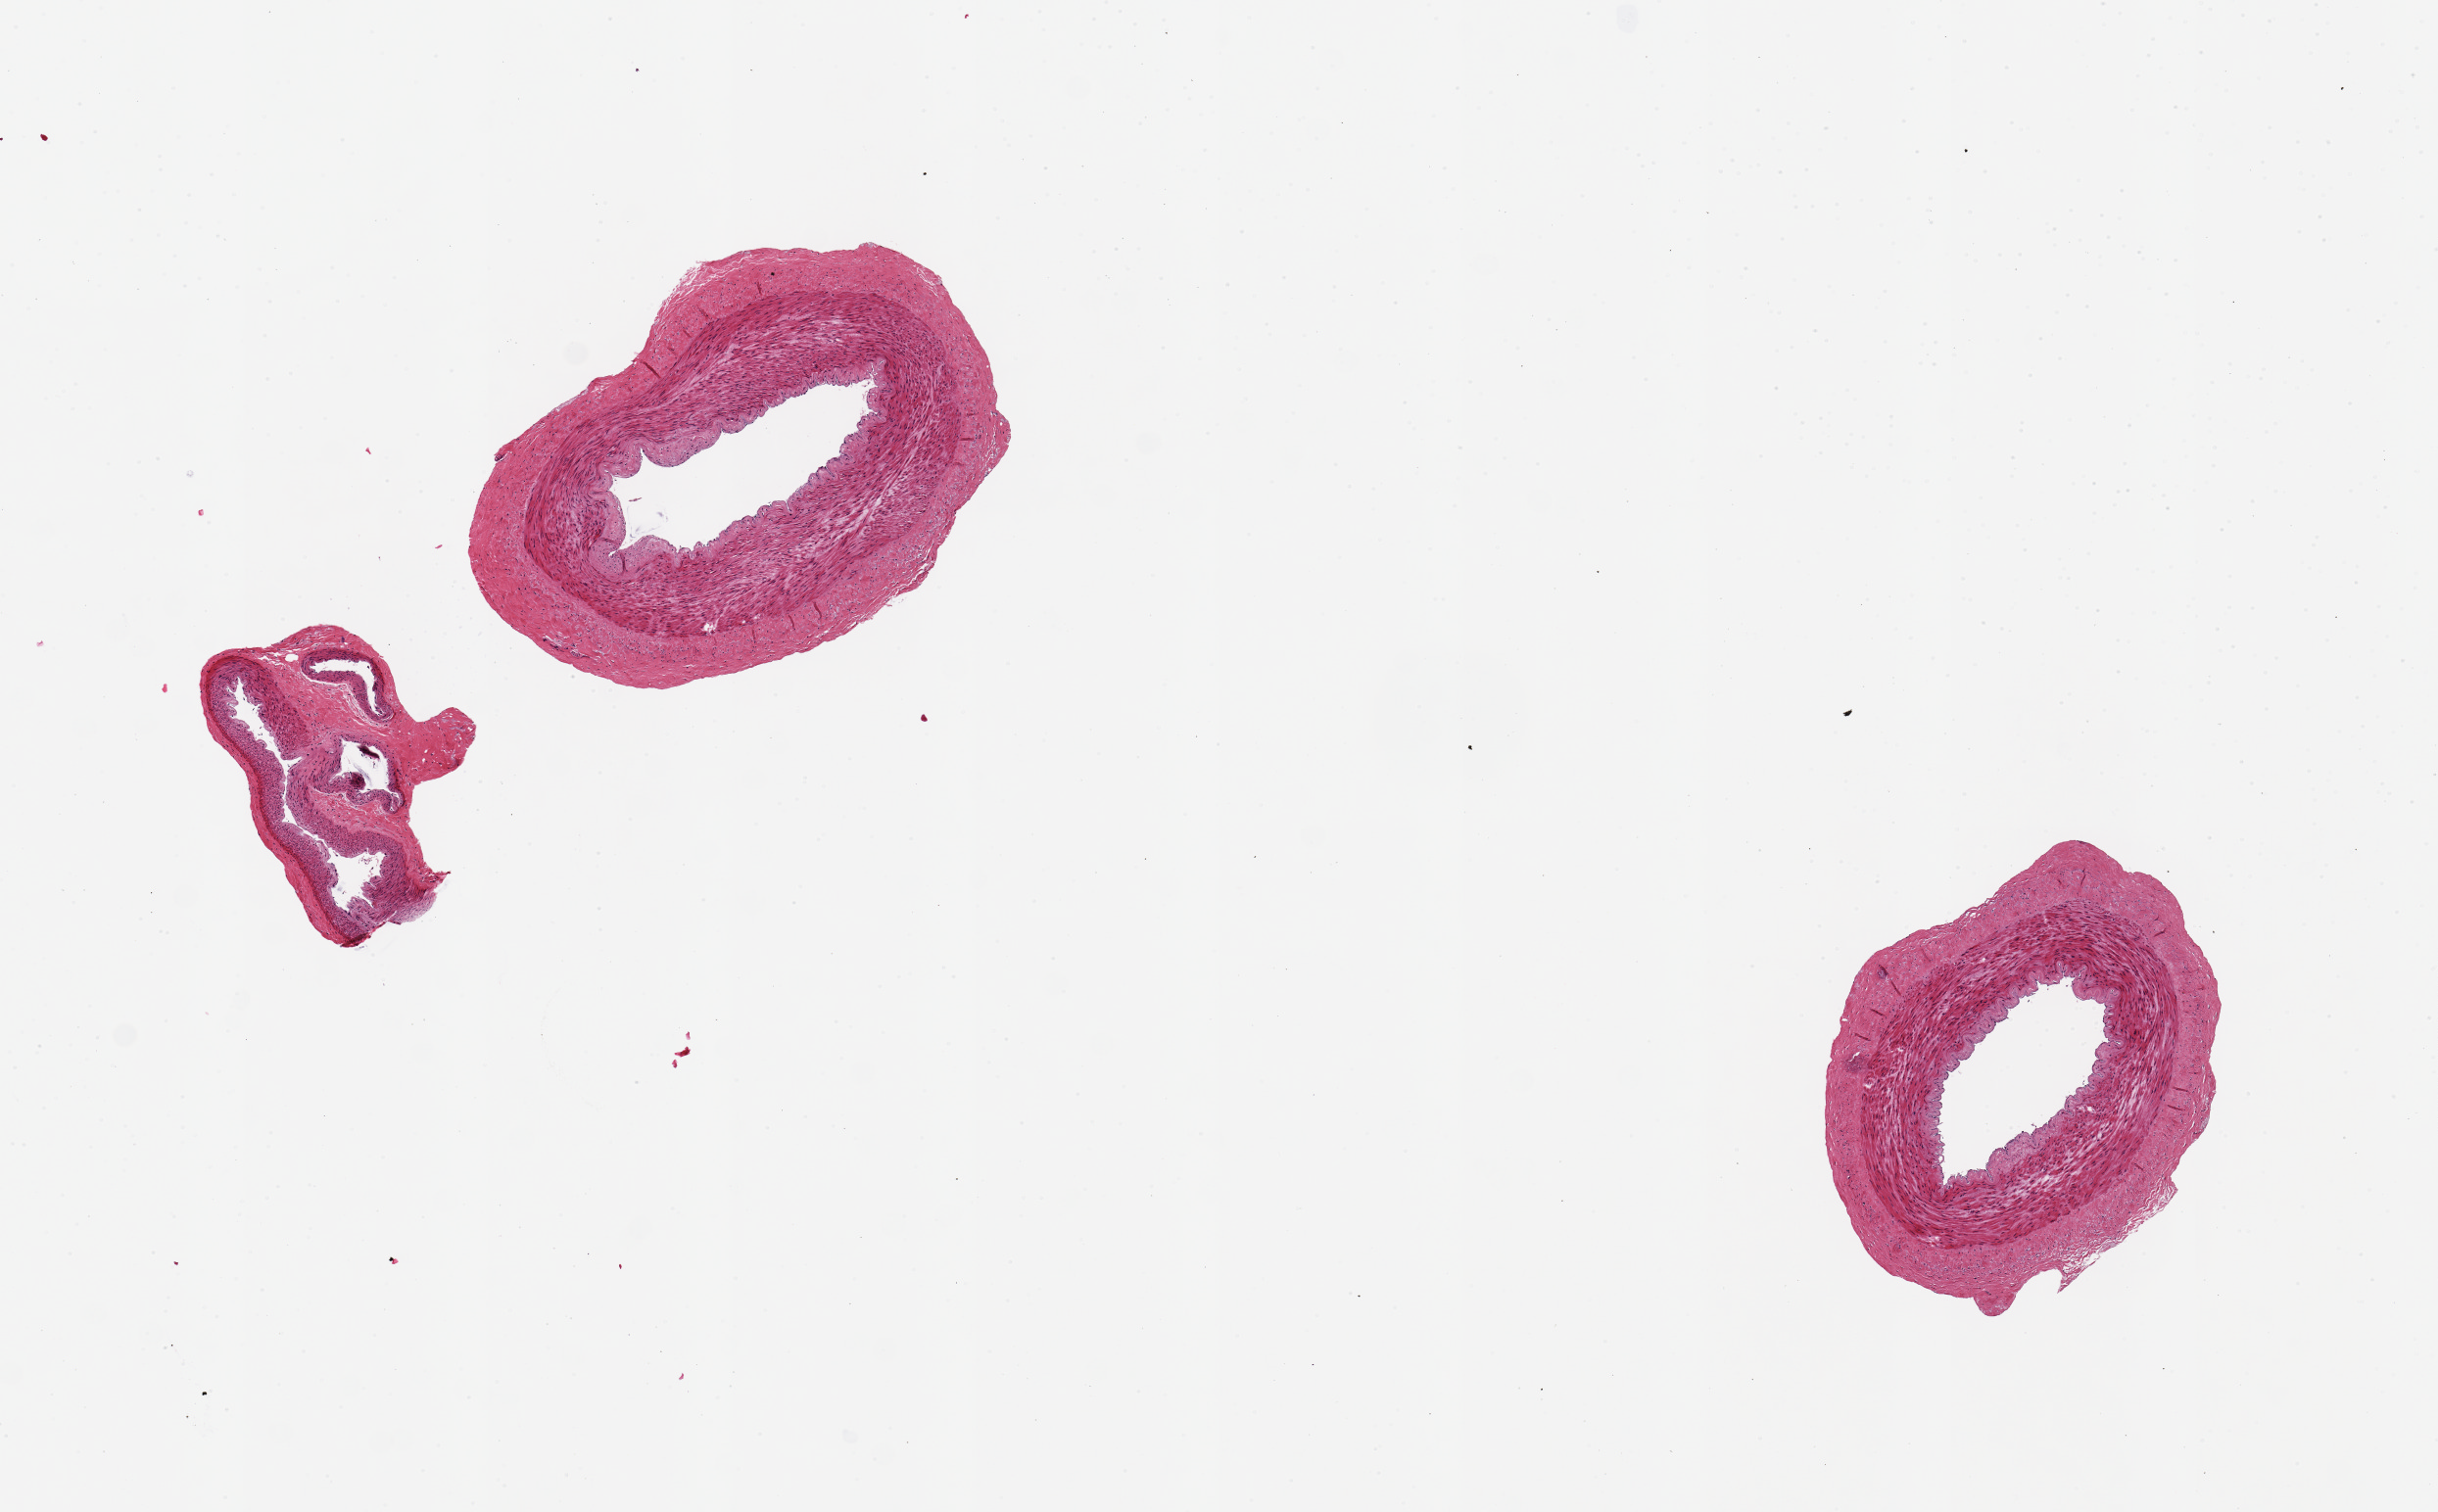
Digitized haematoxylin and eosin-stained section, brightfield, low-resolution overview of the scanned area, about 9.8 x 6.1 mm, PAXgene-fixed paraffin-embedded (PFPE) section, section of tibial artery (target tissue), donor tissue sample. Donor sex: female.
Reviewer comment on this tissue sample: 2 ~2.5x1.5mm aliquots.